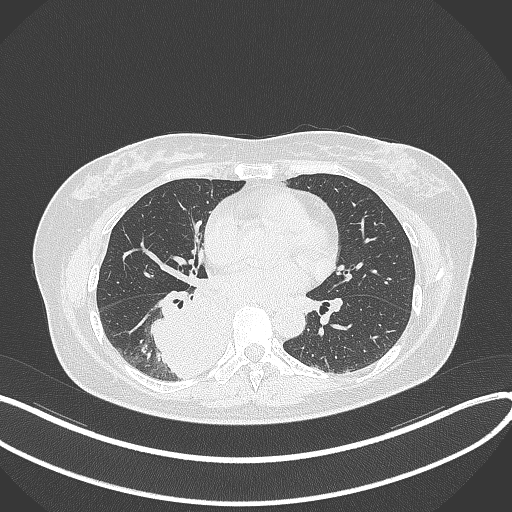
Chest CT, one axial slice. Slice 166 of 331 in the series (ordered by position). Reconstruction kernel B70f. 120 kVp. Lung window (W 1500 / L -600 HU). 1 mm slice thickness. 512 × 512 image matrix, field of view 400 × 400 mm. Female patient, age 54 years. Case-level facts recorded for this patient, not image findings: clinical TNM (as recorded): T4 N0 M0.
Outlined on this slice (bounding box drawn by a radiologist):
- lung tumour (recorded histology: adenocarcinoma): bounding box <145,289,219,382> (left, top, right, bottom; pixels)